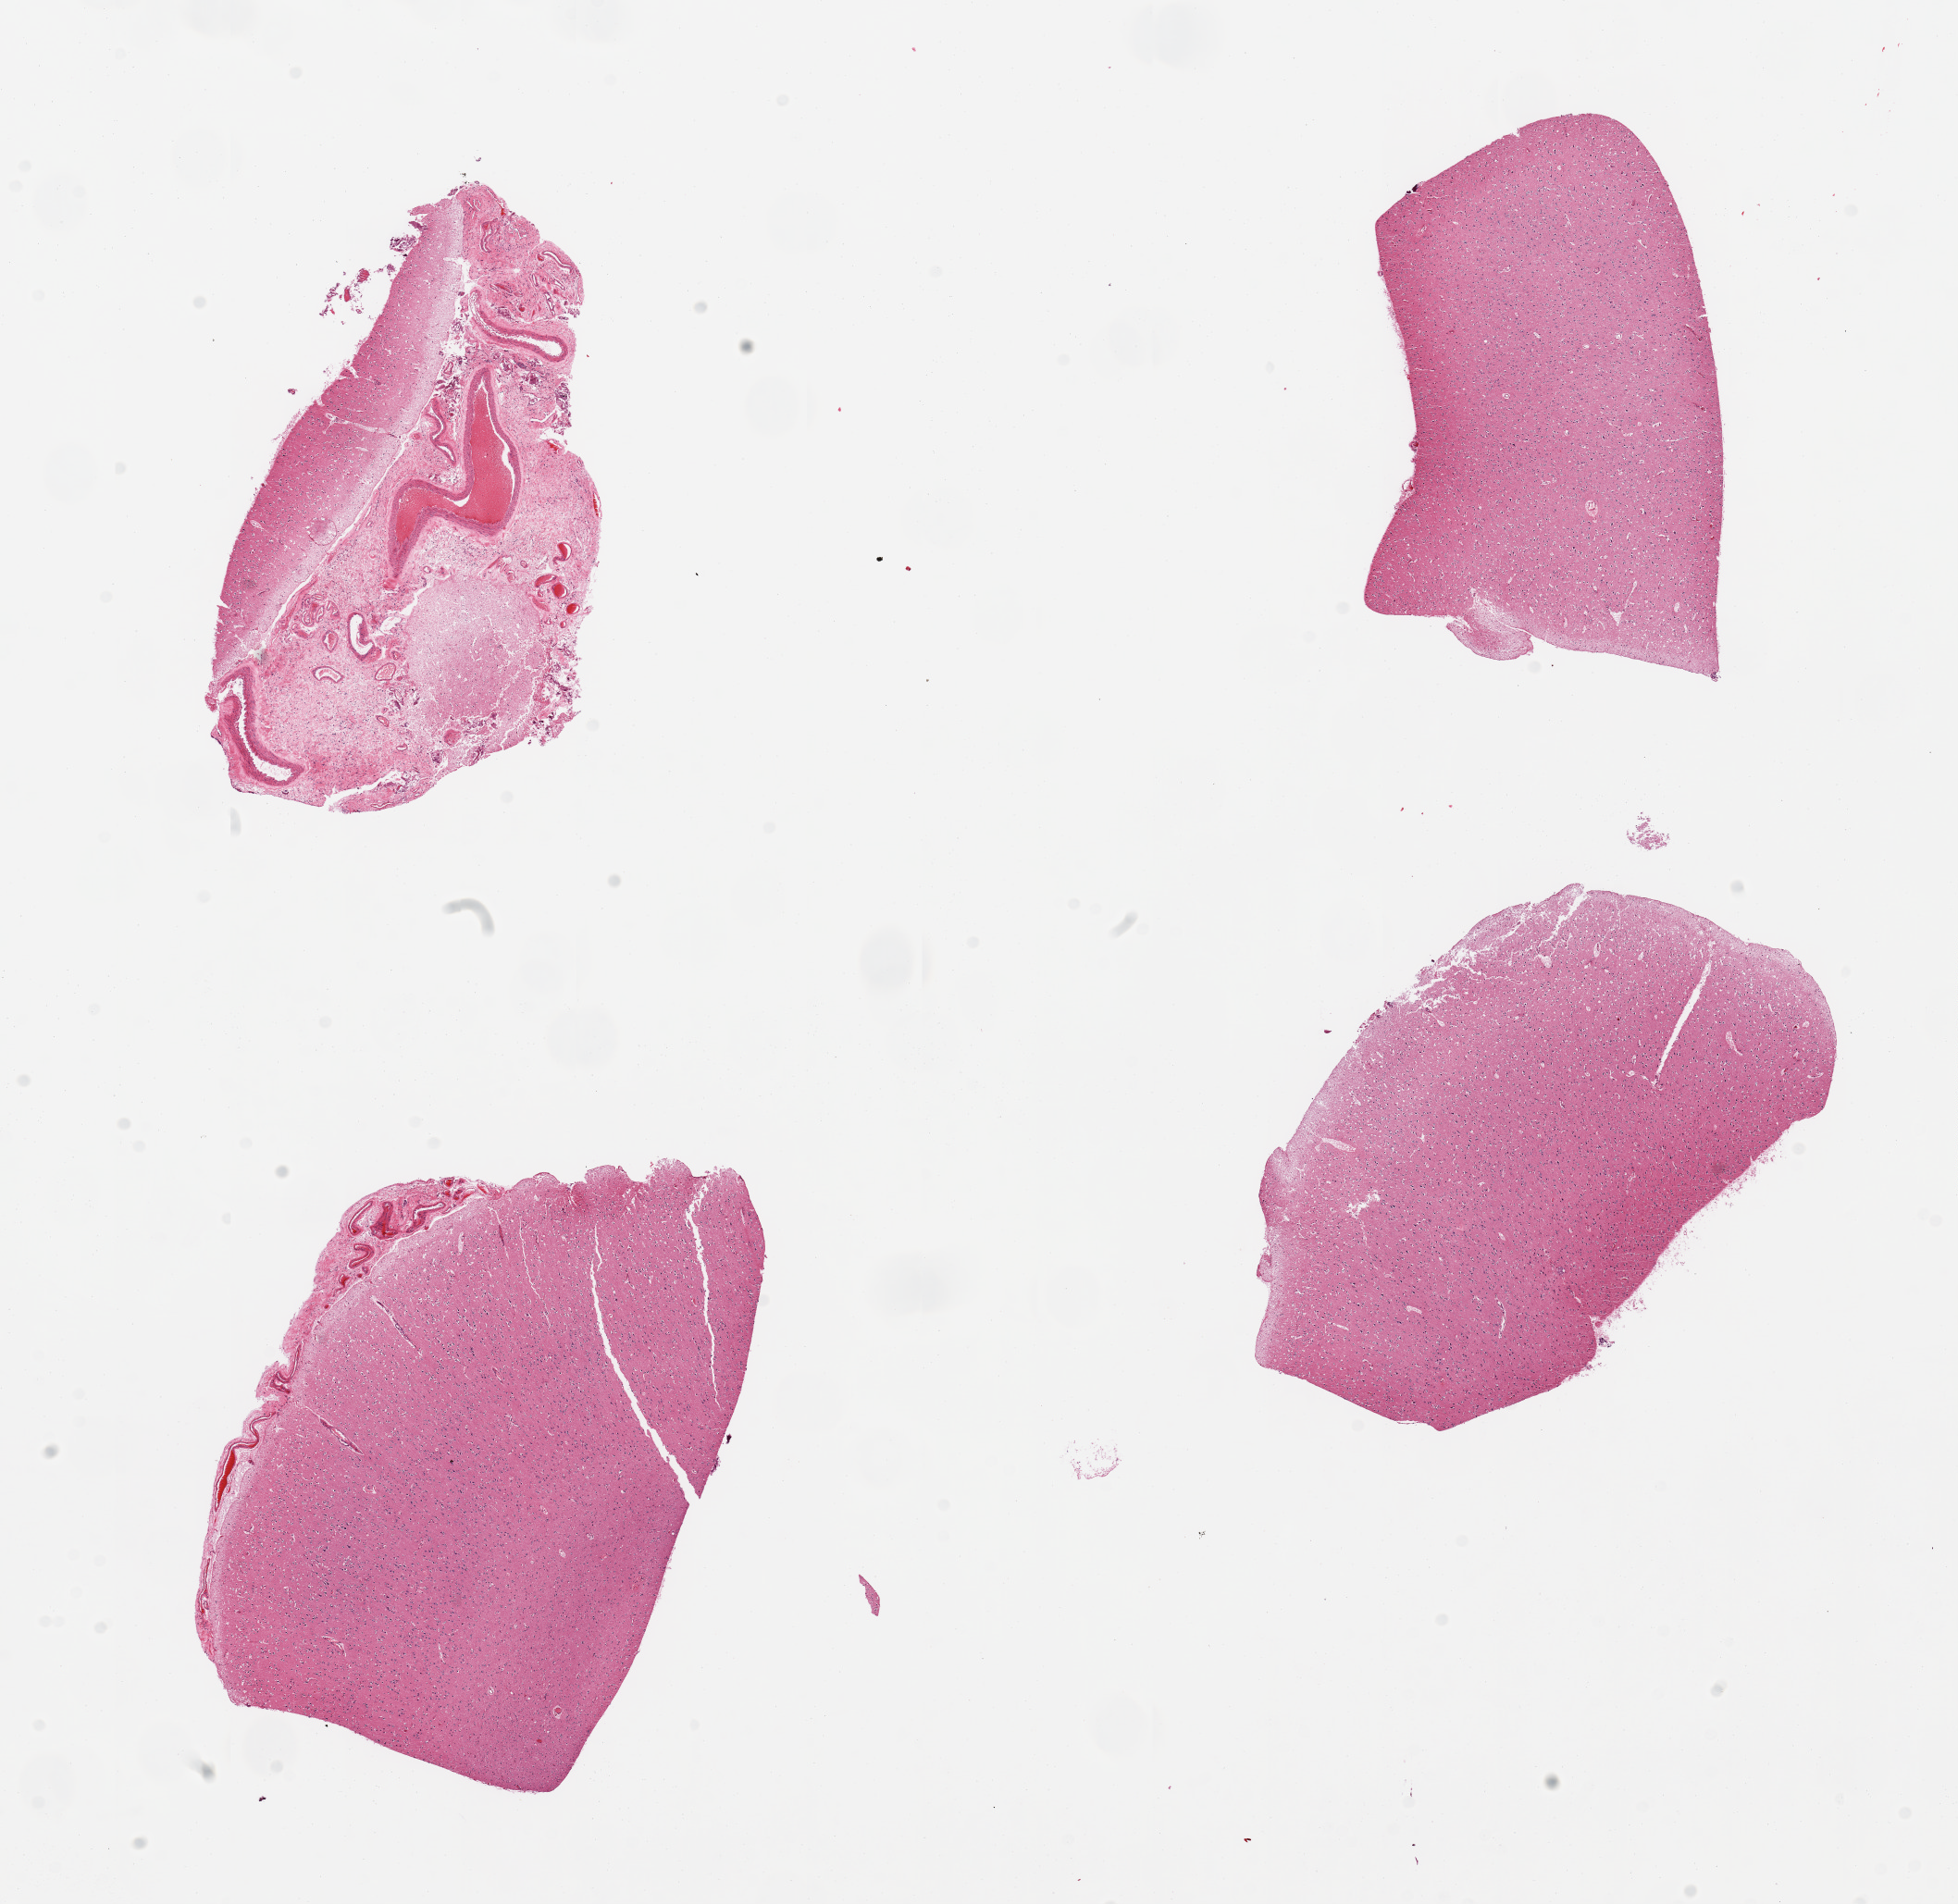
Whole-slide image, haematoxylin and eosin stain — a low-resolution overview of the entire scanned area, about 16.7 x 16.3 mm (from a 20x scan), PAXgene-fixed, paraffin-embedded tissue, sampled site (target tissue): cerebral cortex, tissue donor sample. Donor sex: male.
Pathologist's review note for this sample: 4 pieces, includes adherent meninges.